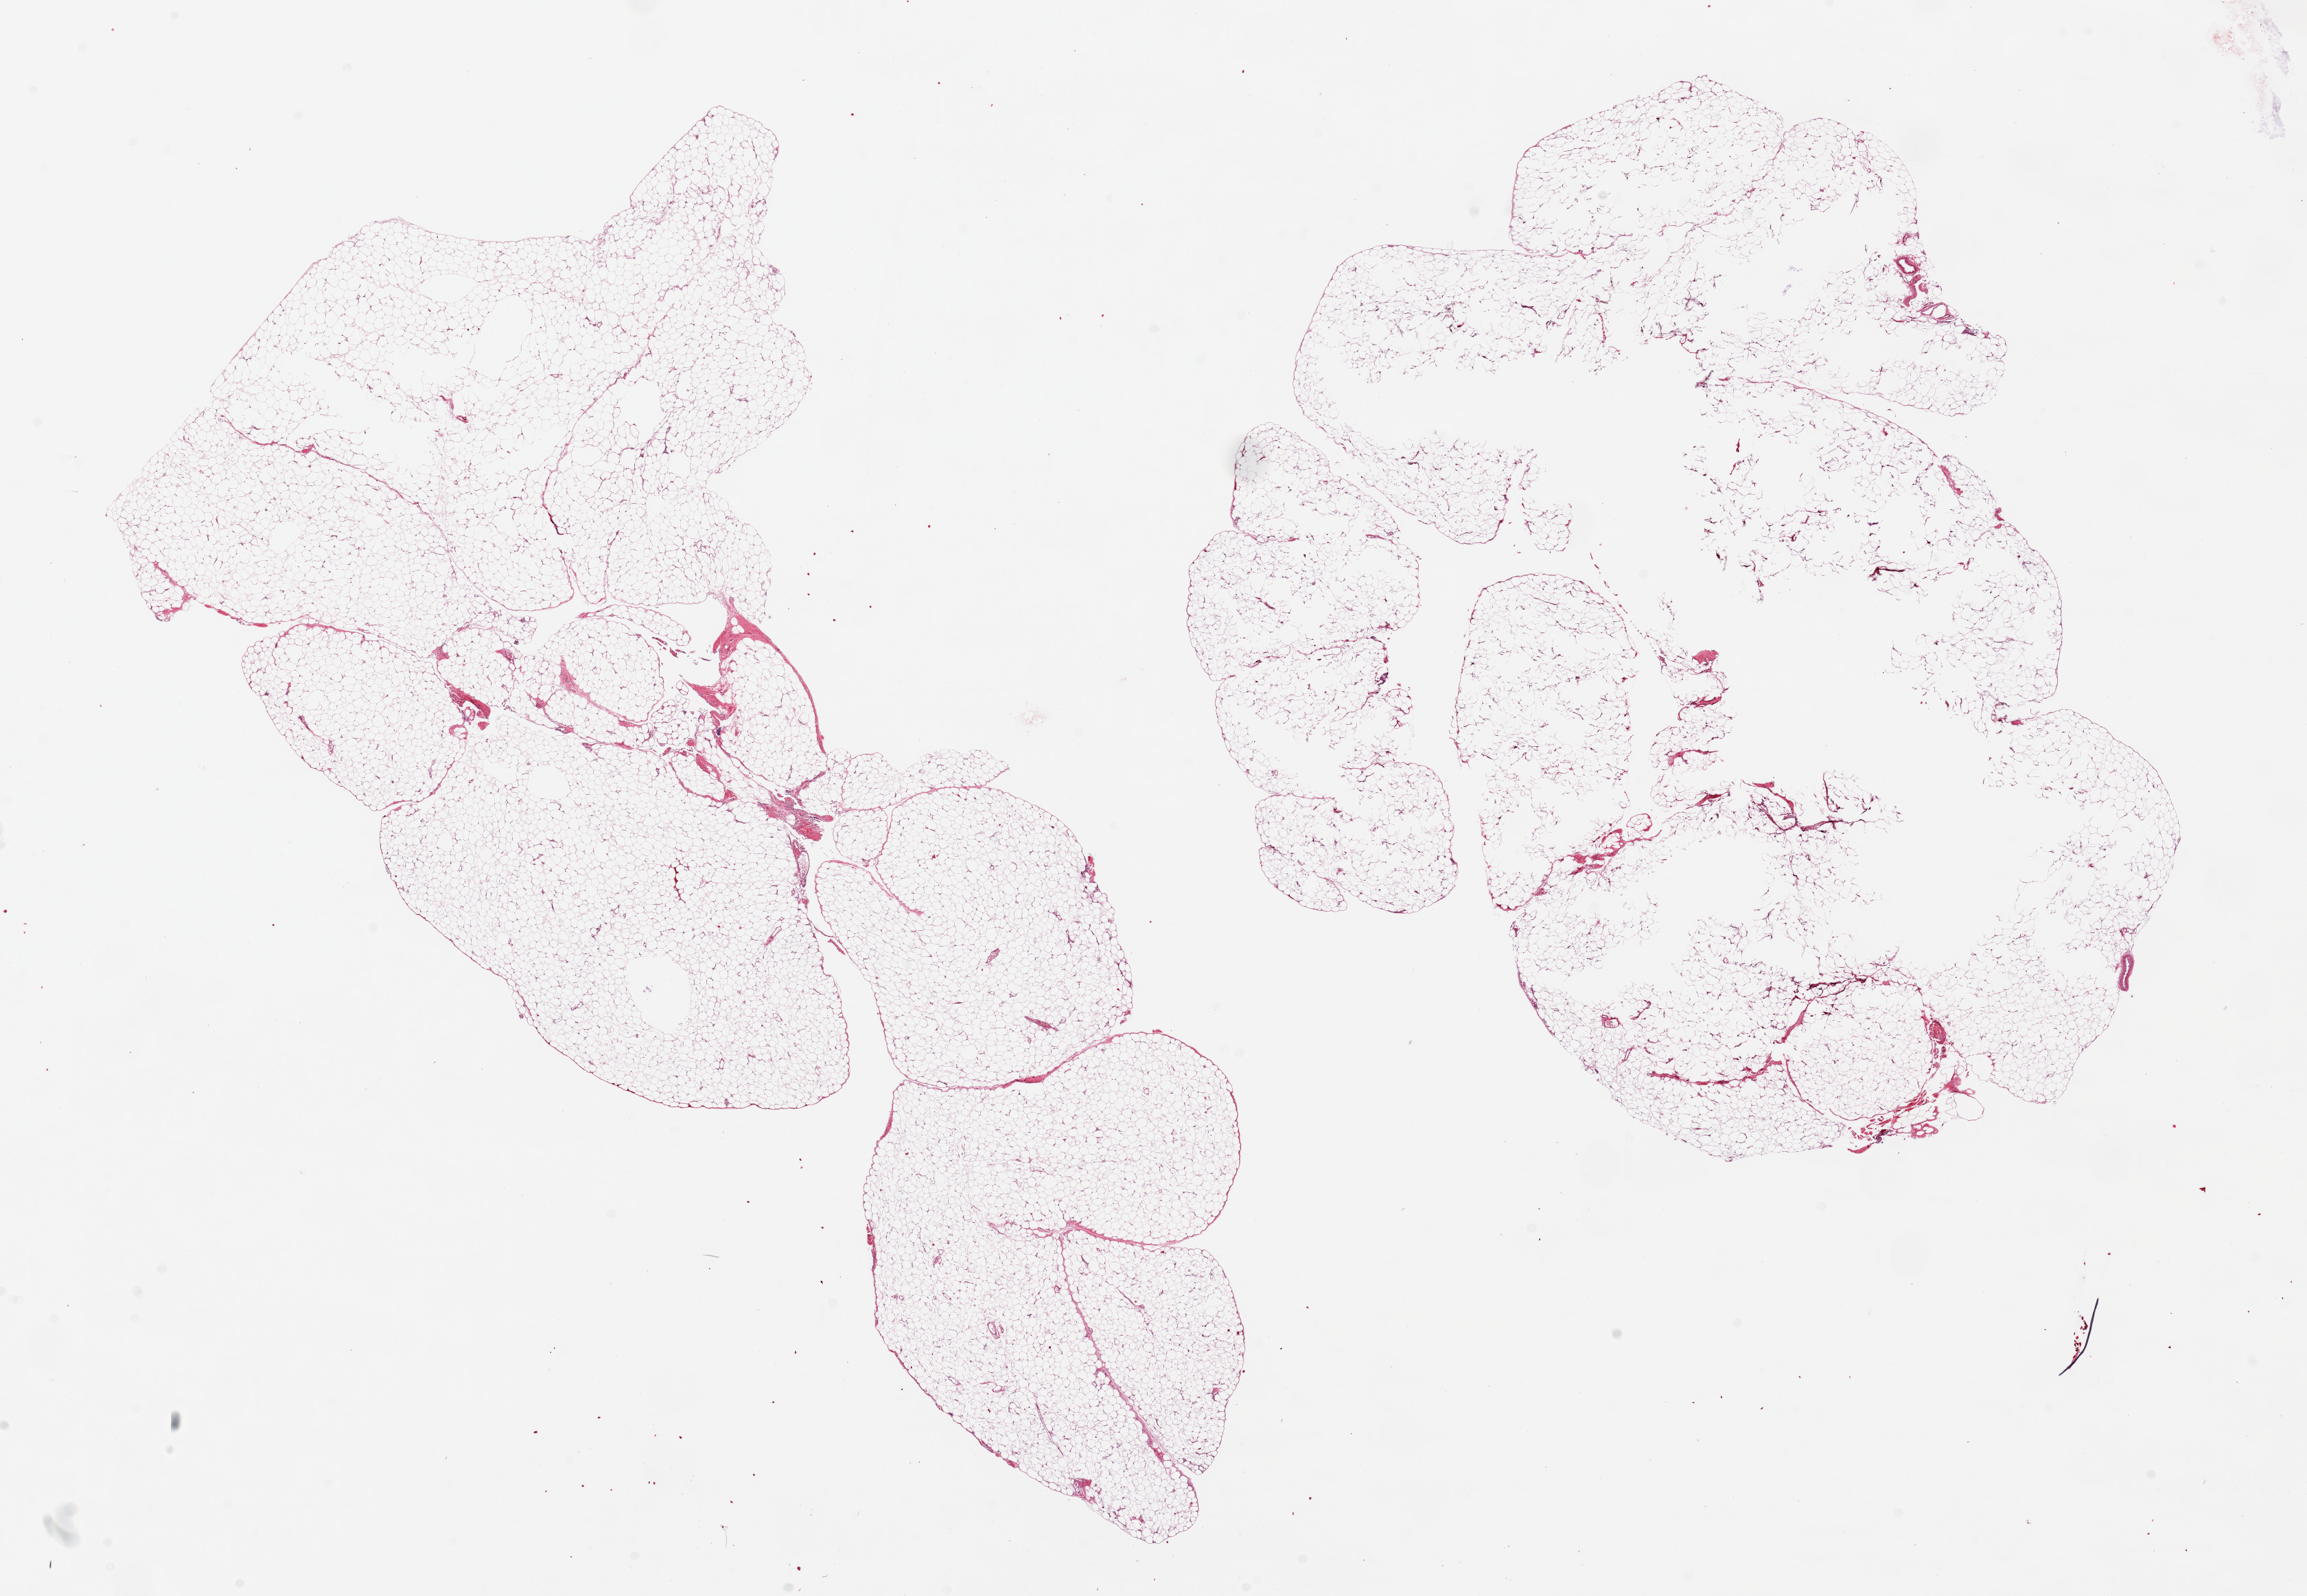
H&E whole-slide image, brightfield, whole scanned area (about 26.6 x 18.4 mm) shown as a low-resolution overview, PAXgene-fixed paraffin-embedded (PFPE) section, target tissue: omentum, tissue donor sample.
* review note (as recorded): 2 pieces ~14.x9mm